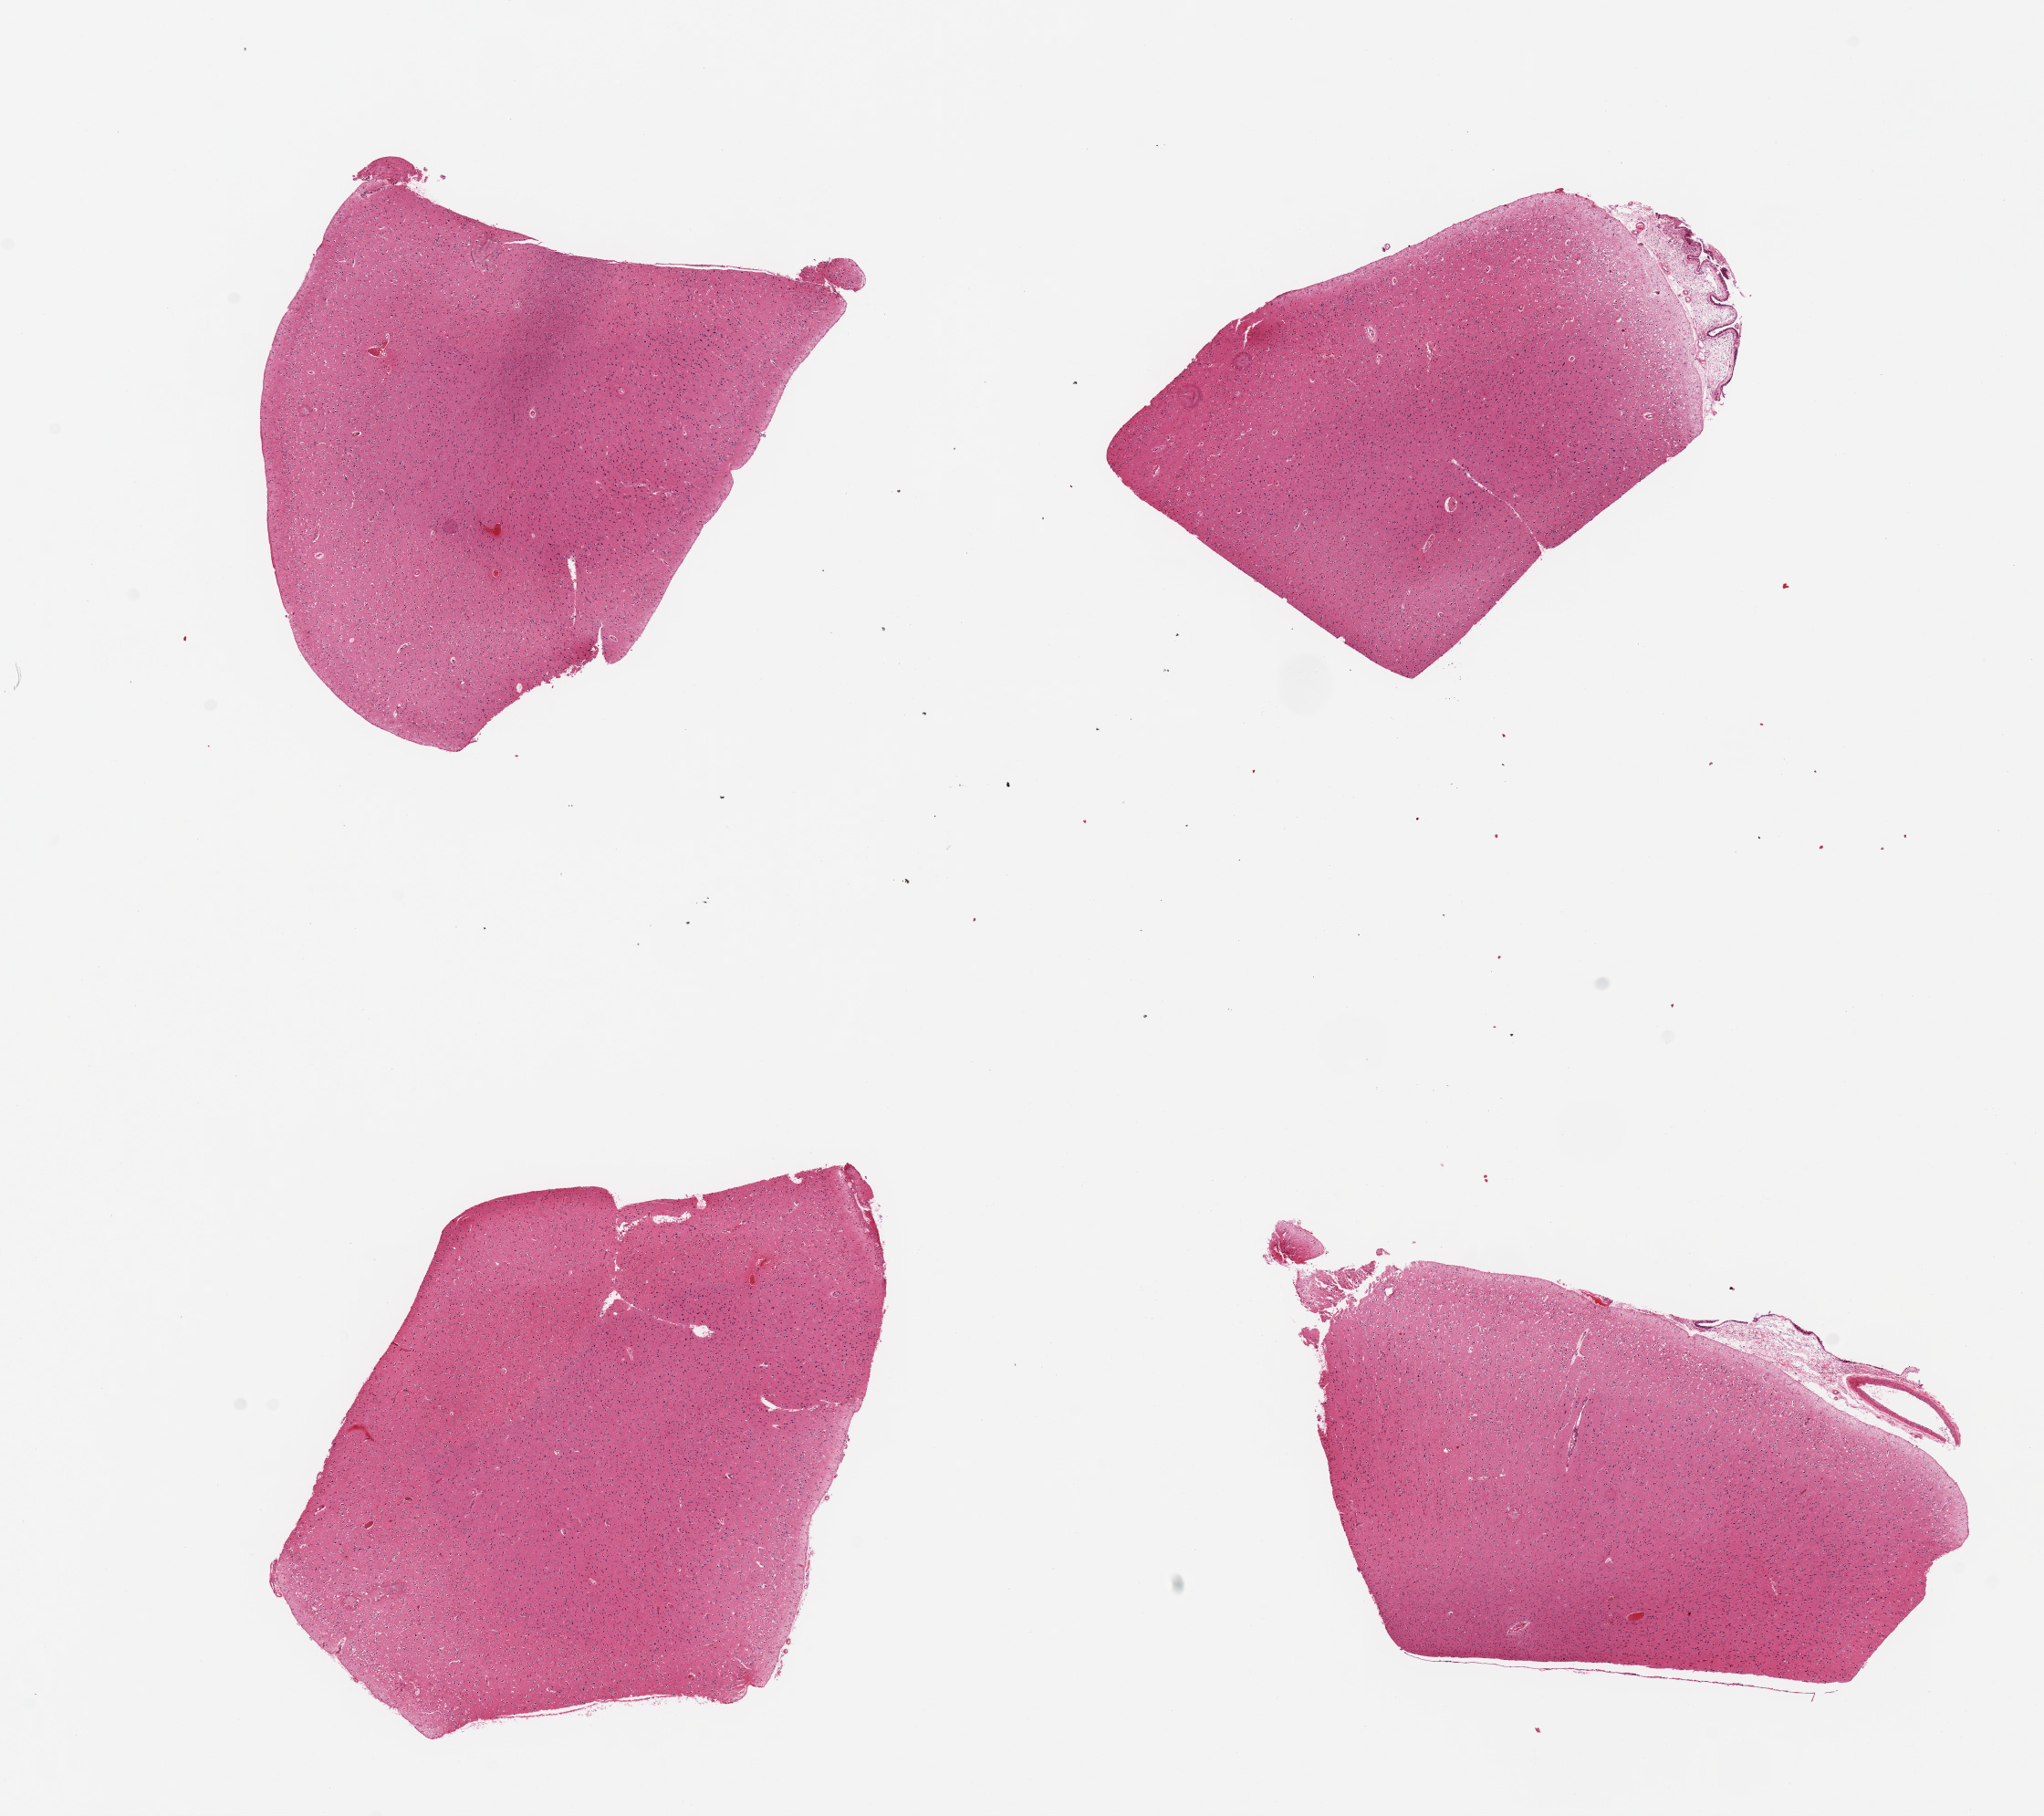
Whole-slide image, haematoxylin and eosin stain, brightfield, shown as a low-resolution overview of the whole scanned area (about 17.7 x 15.7 mm). PAXgene-fixed, paraffin-embedded tissue. Section of cerebral cortex (target tissue). Tissue donor sample. Donor: female.
Reviewer comment on this tissue sample: 4 pieces, no abnormalities; fragment of dura/choroid plexus.